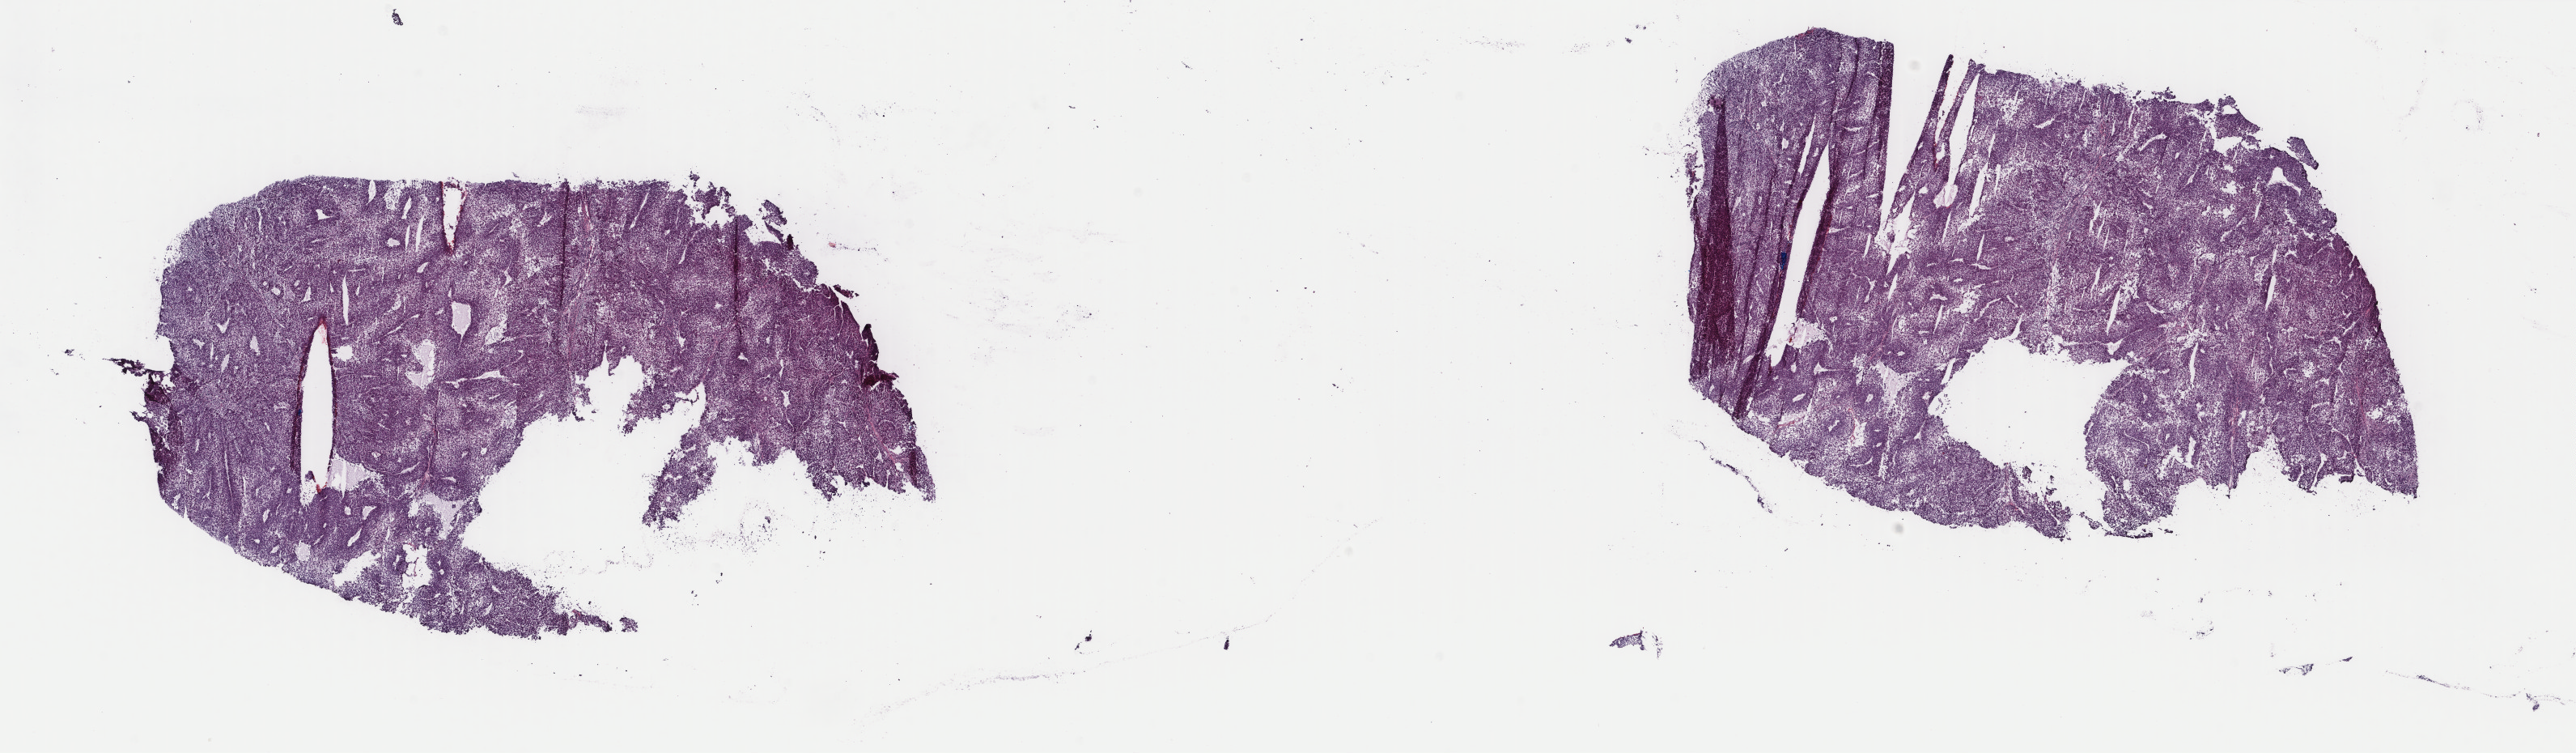
Whole-slide histology image, Hematoxylin and eosin (H&E) stained, low-resolution overview of the scanned area, about 25.3 x 7.4 mm (acquisition: 40x scan); frozen section from the top of the tissue portion; primary tumour sample from the liver. Patient: male, age at initial diagnosis 52 years. Histologic grade: G2 (moderately differentiated). Composition of this section per pathologist review: tumour cells 75%, tumour nuclei 75%, normal cells 0%, stromal cells 21%, necrosis 4%. Inflammatory infiltration, as recorded: lymphocyte infiltration 2%, monocyte infiltration 1%, neutrophil infiltration 1%.
- pathologic diagnosis: Hepatocellular carcinoma, NOS
- AJCC pathologic stage: I (7th edition)